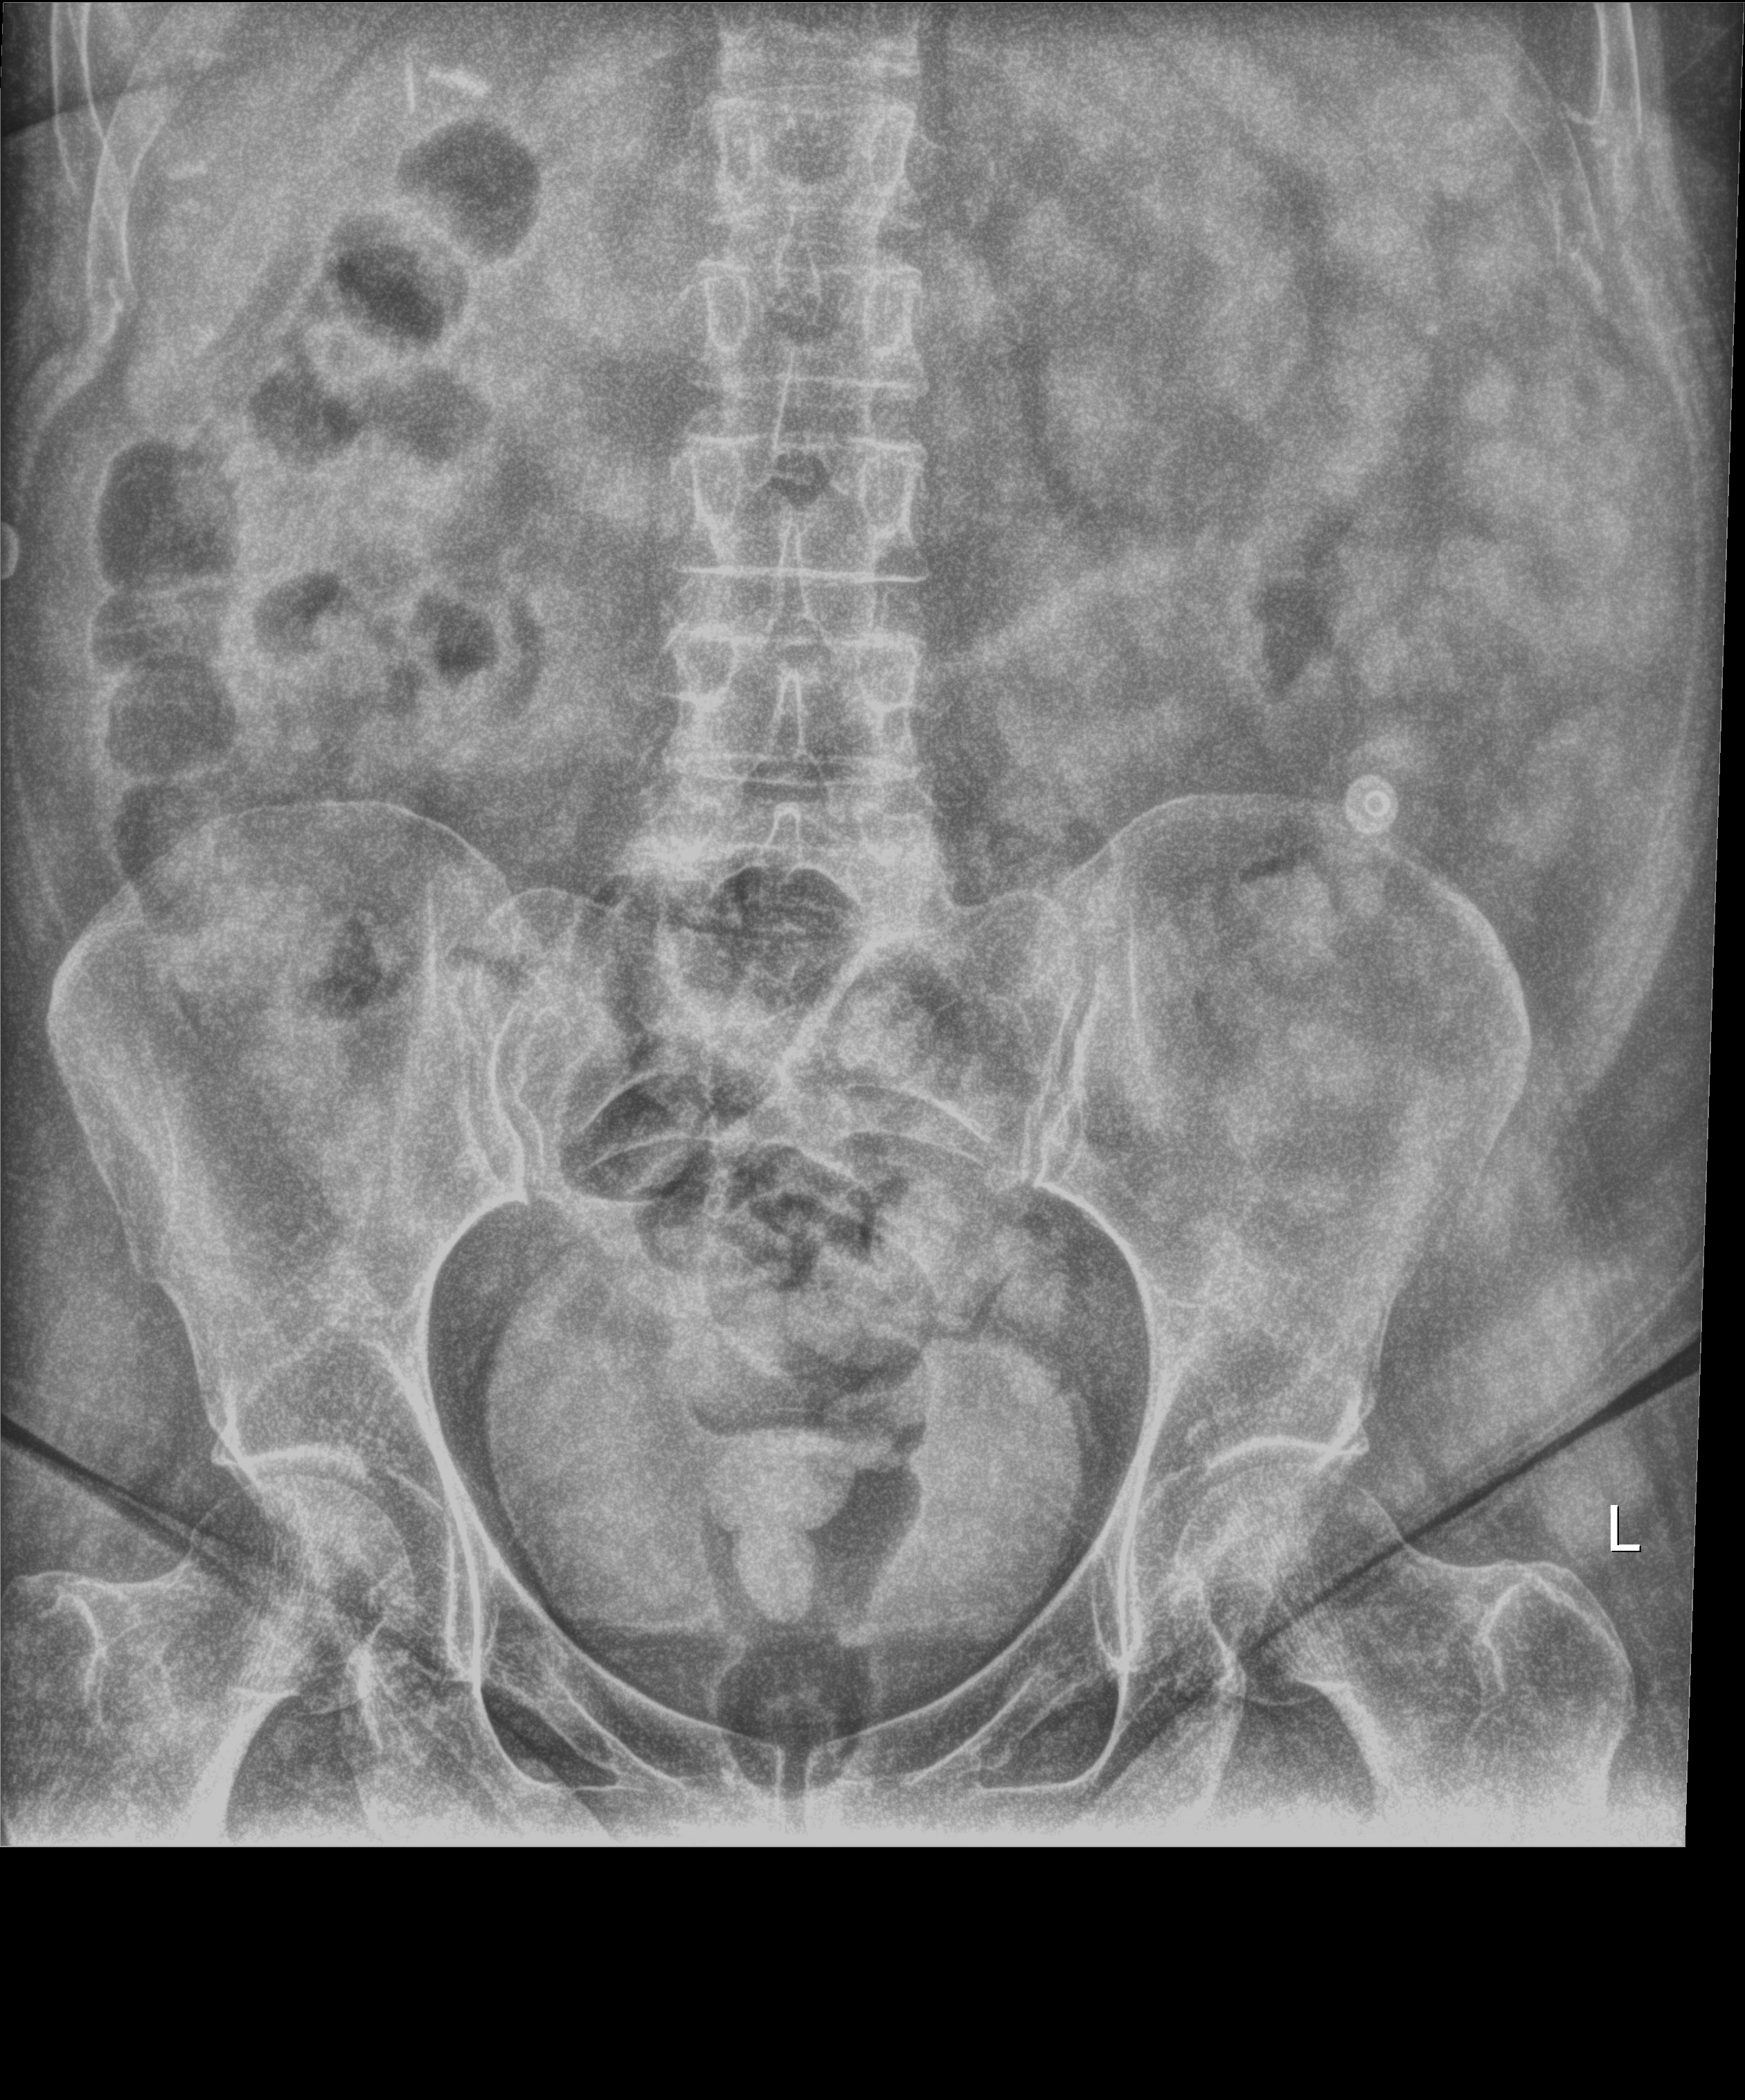
Bedside abdomen radiograph (digital radiography); anteroposterior (AP) projection. Patient hospitalised with COVID-19; female, aged 18–59 years.
From the hospital-stay record, not from the radiograph (when in the stay this image was taken is not recorded):
- mechanically ventilated during this hospital stay: no
- length of hospital stay: 44 days